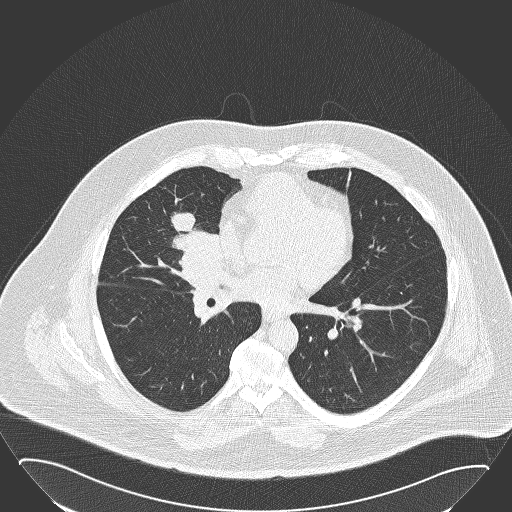
Low-dose screening chest CT, one axial slice. Slice 78 of 168 in the series (ordered by position). 120 kVp. Lung window (W 1500 / L -600 HU). 2 mm slice thickness. 512 × 512 image matrix, field of view 432 × 432 mm.
Structures marked on this image (expert manual segmentation):
- lesion 1 (tumor, hilum of right lung): box from (x=171, y=213) to (x=223, y=284) px